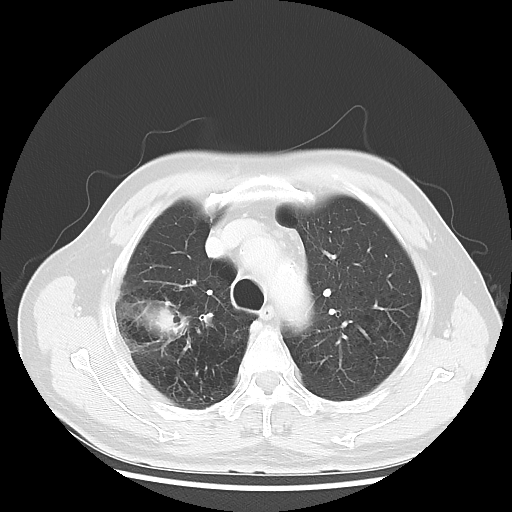
Chest CT, one axial slice; position 38 of 50 along the scan axis; reconstruction kernel LUNG; 120 kVp; lung window (W 1500 / L -600 HU); 512 × 512 image matrix, field of view 360 × 360 mm. Male patient, age 69 years. Case-level facts recorded for this patient, not image findings: clinical TNM (as recorded): T3 N0 M0.
Annotated regions visible in this slice (rectangle marked by the reading radiologist):
- lung tumour (recorded histology: adenocarcinoma): box from (x=115, y=289) to (x=193, y=354) px